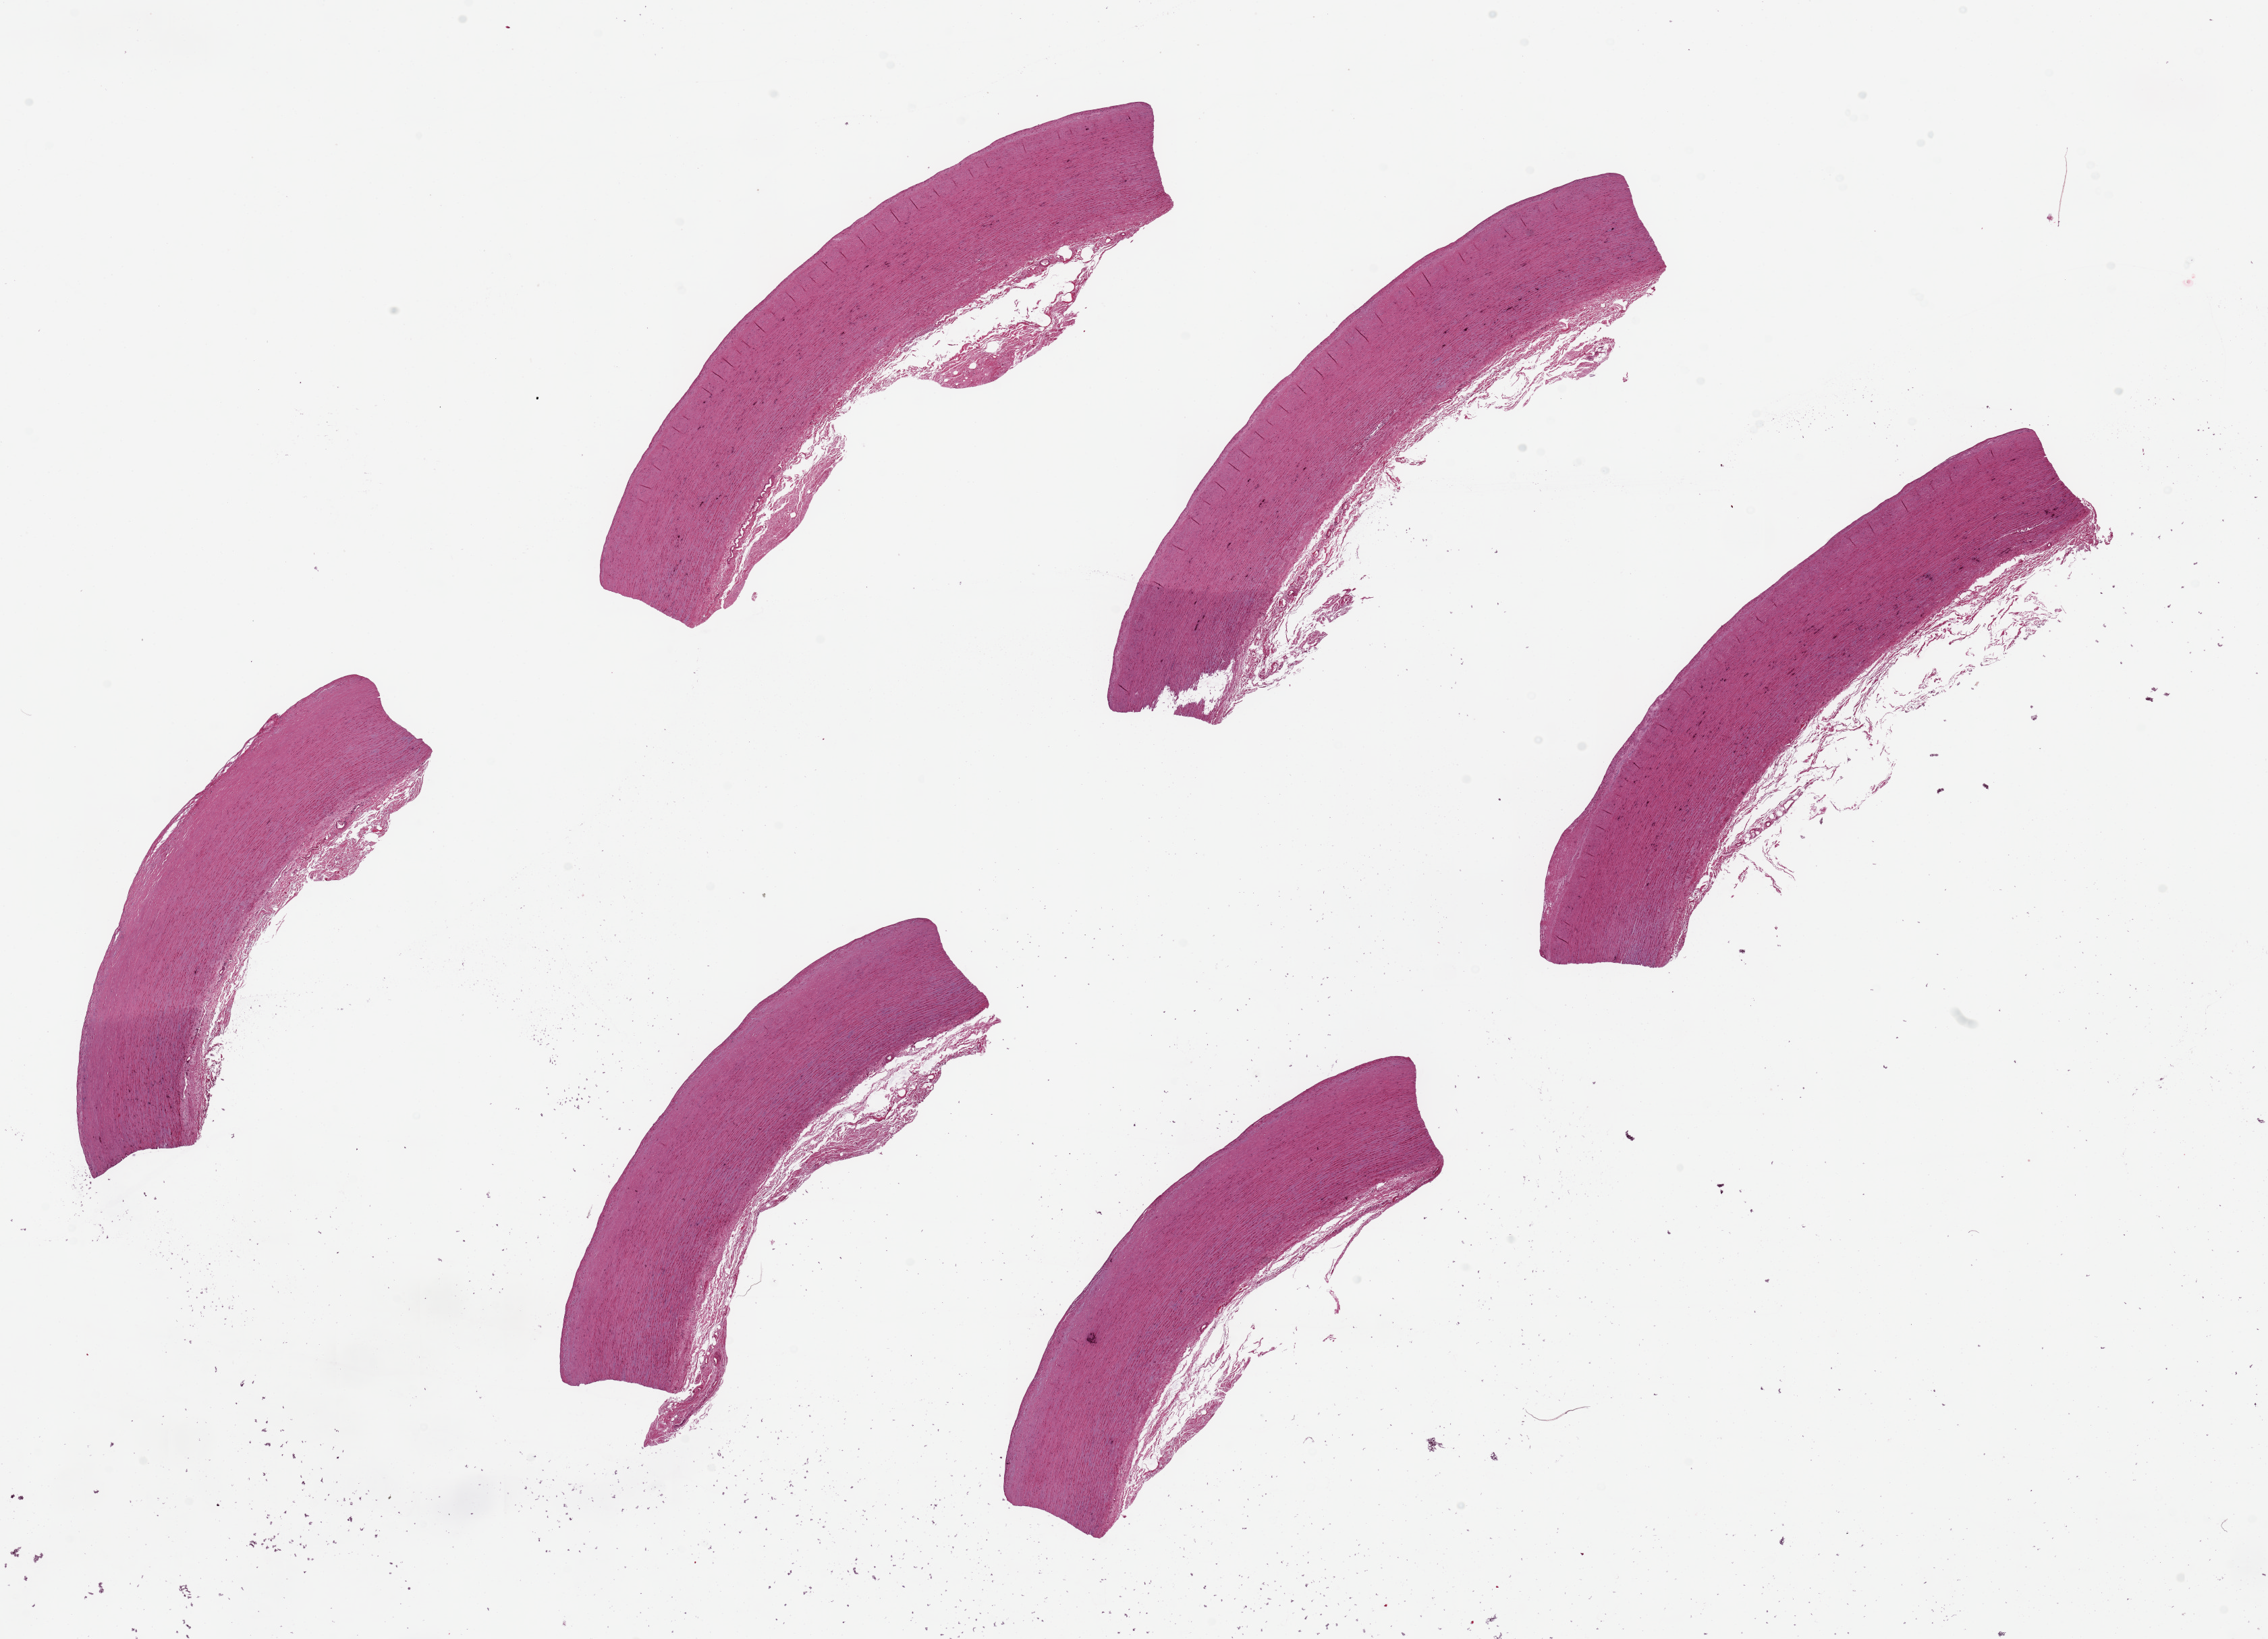
Haematoxylin and eosin whole-slide image — whole scanned area (about 26.6 x 19.2 mm, acquisition: 20x scan) shown as a low-resolution overview, PAXgene-fixed paraffin-embedded (PFPE) section, sampled site (target tissue): aorta, tissue donor sample.
Reviewer comment on this tissue sample: 6 pieces up to 8x2 mm; no plaques.